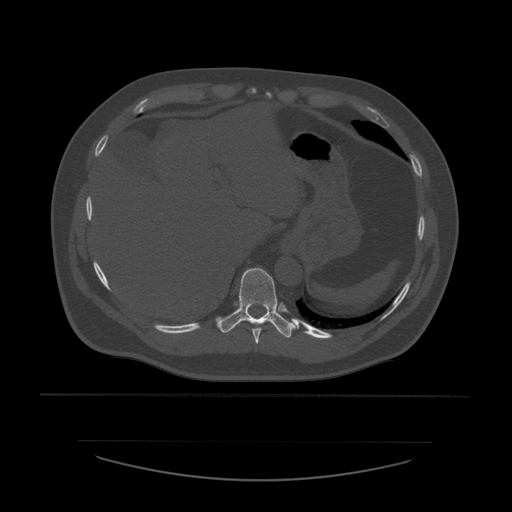
CT including the spine, one axial slice. Position 302 of 532 along the scan axis. Reconstruction kernel STANDARD. 120 kVp. Bone window (W 1800 / L 400 HU). 1.25 mm slice thickness. 512 × 512 image matrix, field of view 441 × 441 mm. Patient age 44 years. From the clinical record (not read from this slice): primary cancer: soft tissue sarcoma.
Structures marked on this image (semi-automatic segmentation, software-assisted and operator-edited):
- T10 vertebra: bounding box (x1, y1, x2, y2) in pixels: (216, 268, 298, 338)
- T9 vertebra: (252, 322, 271, 344)